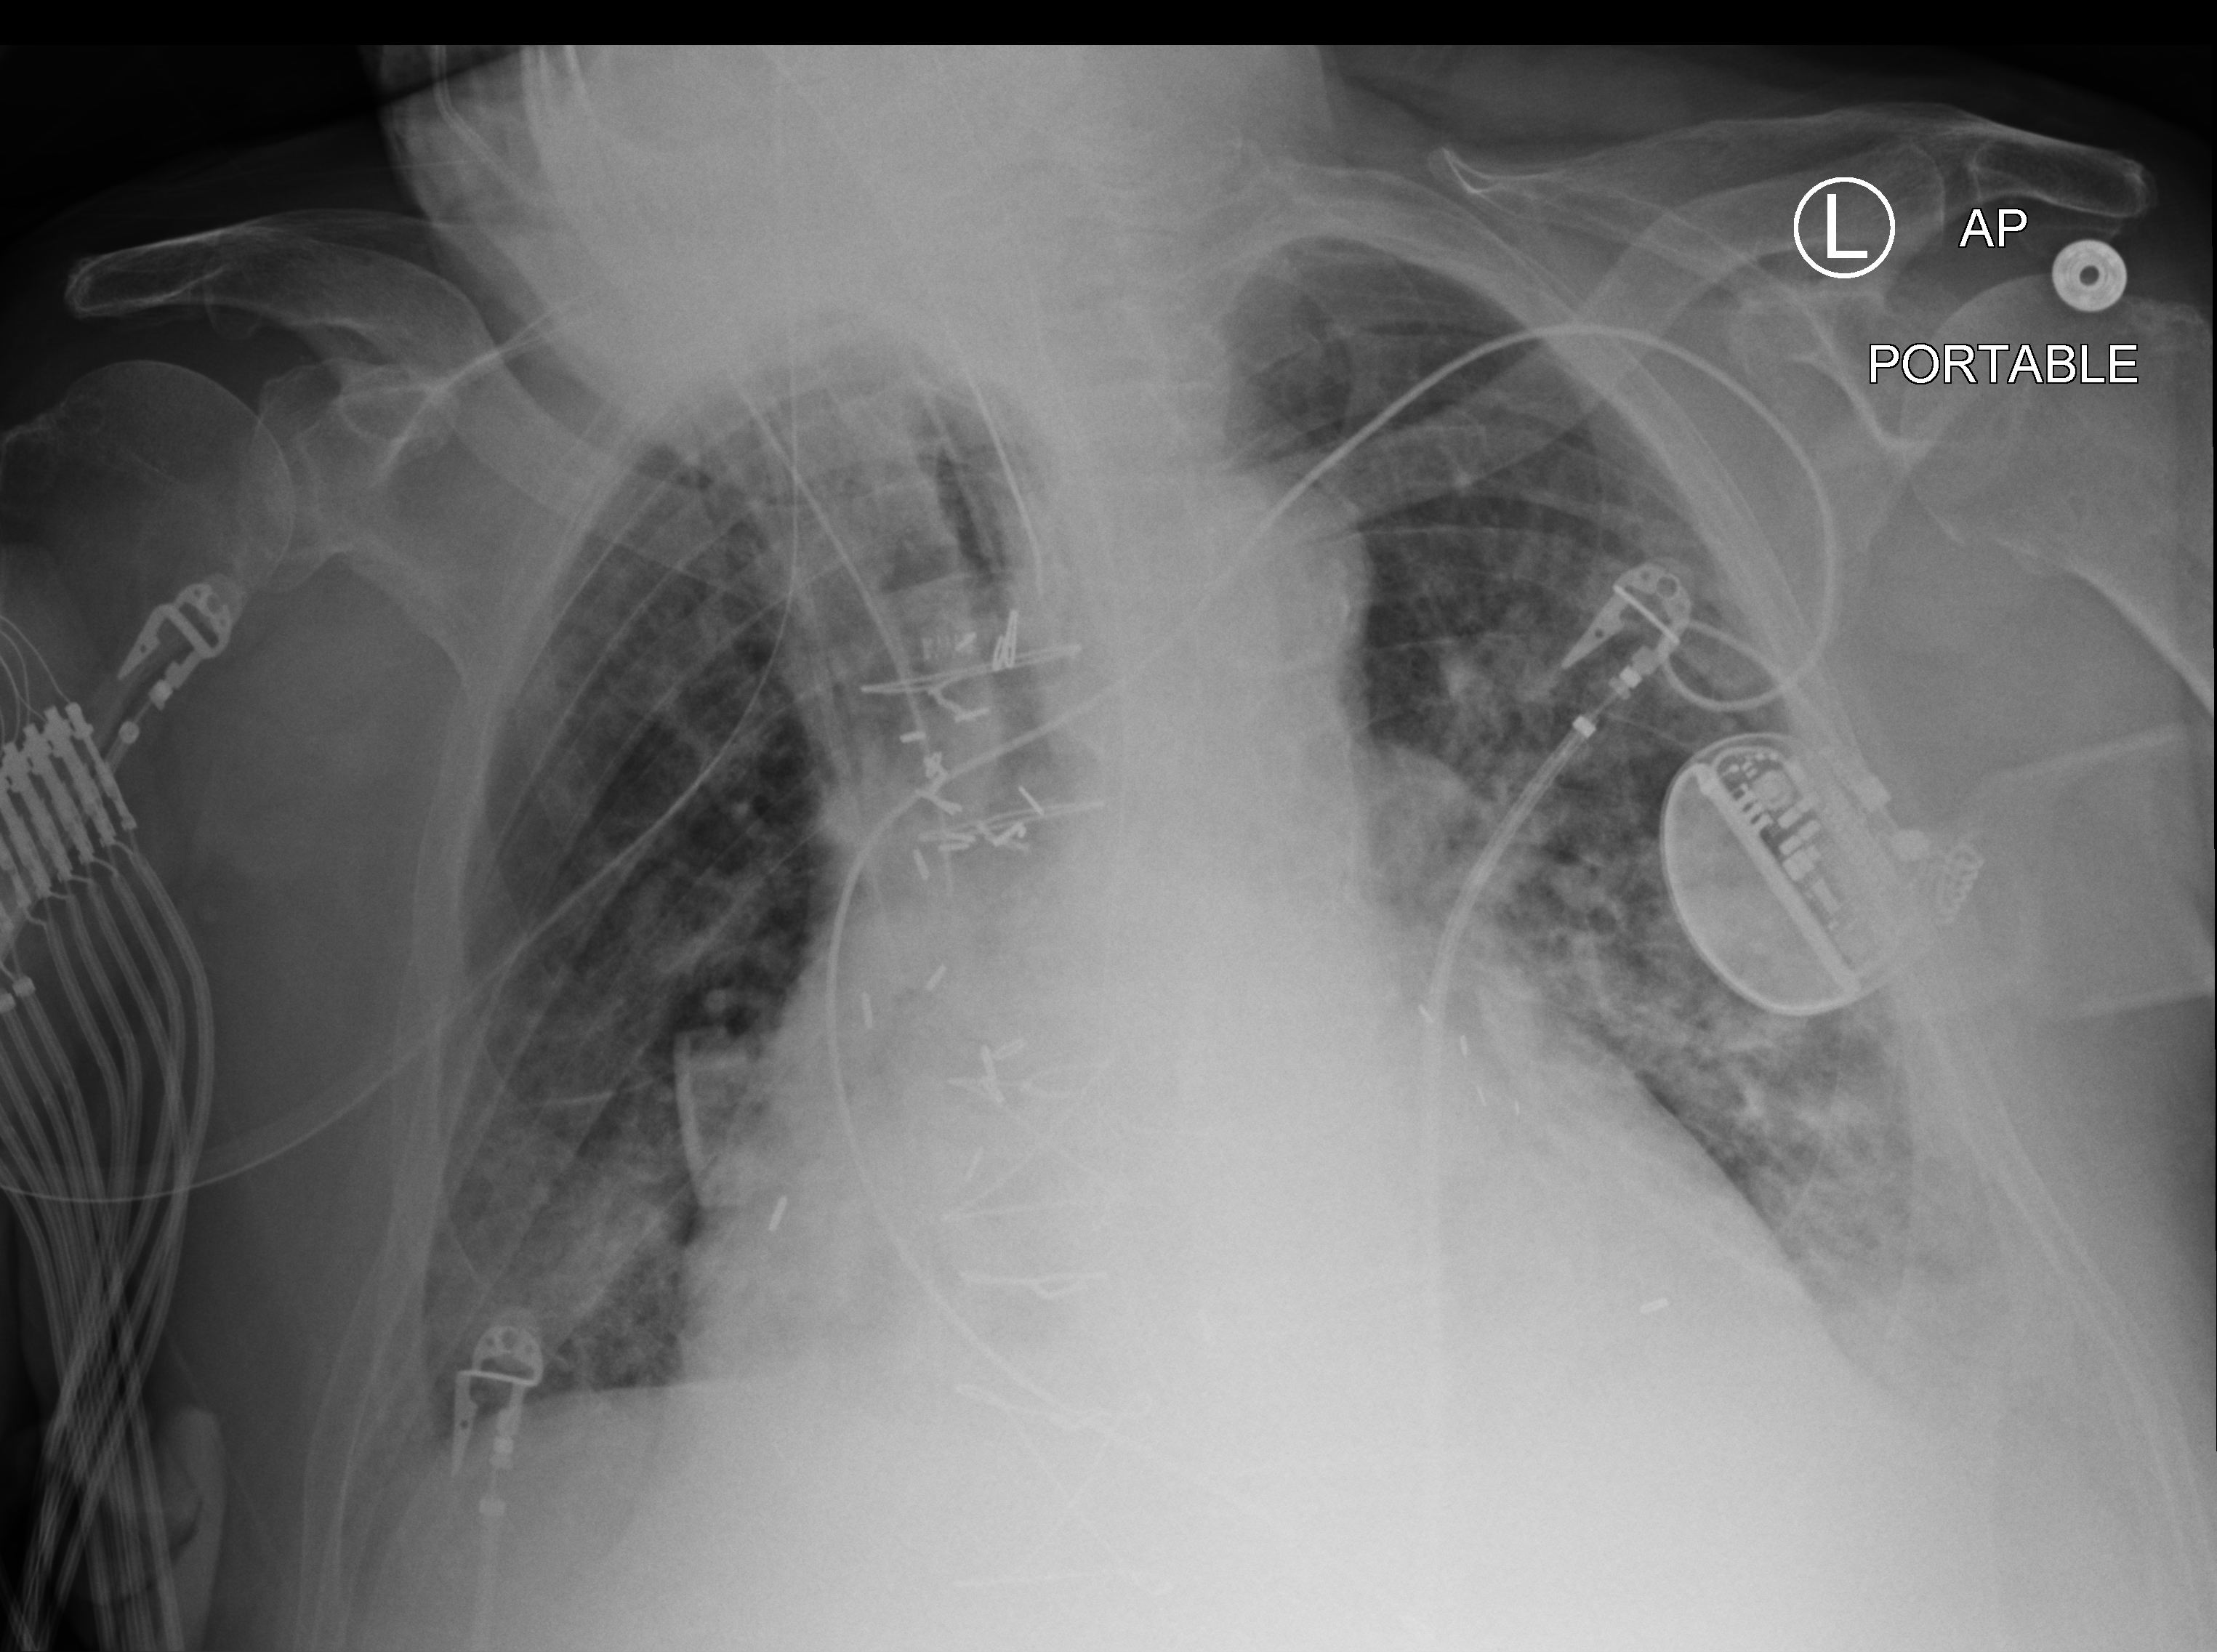
Bedside chest radiograph (computed radiography), anteroposterior (AP) projection. Male patient hospitalised with COVID-19, age 75–90 years.
From the hospital-stay record, not from the radiograph (when in the stay this image was taken is not recorded): hypertension (admission record): yes.